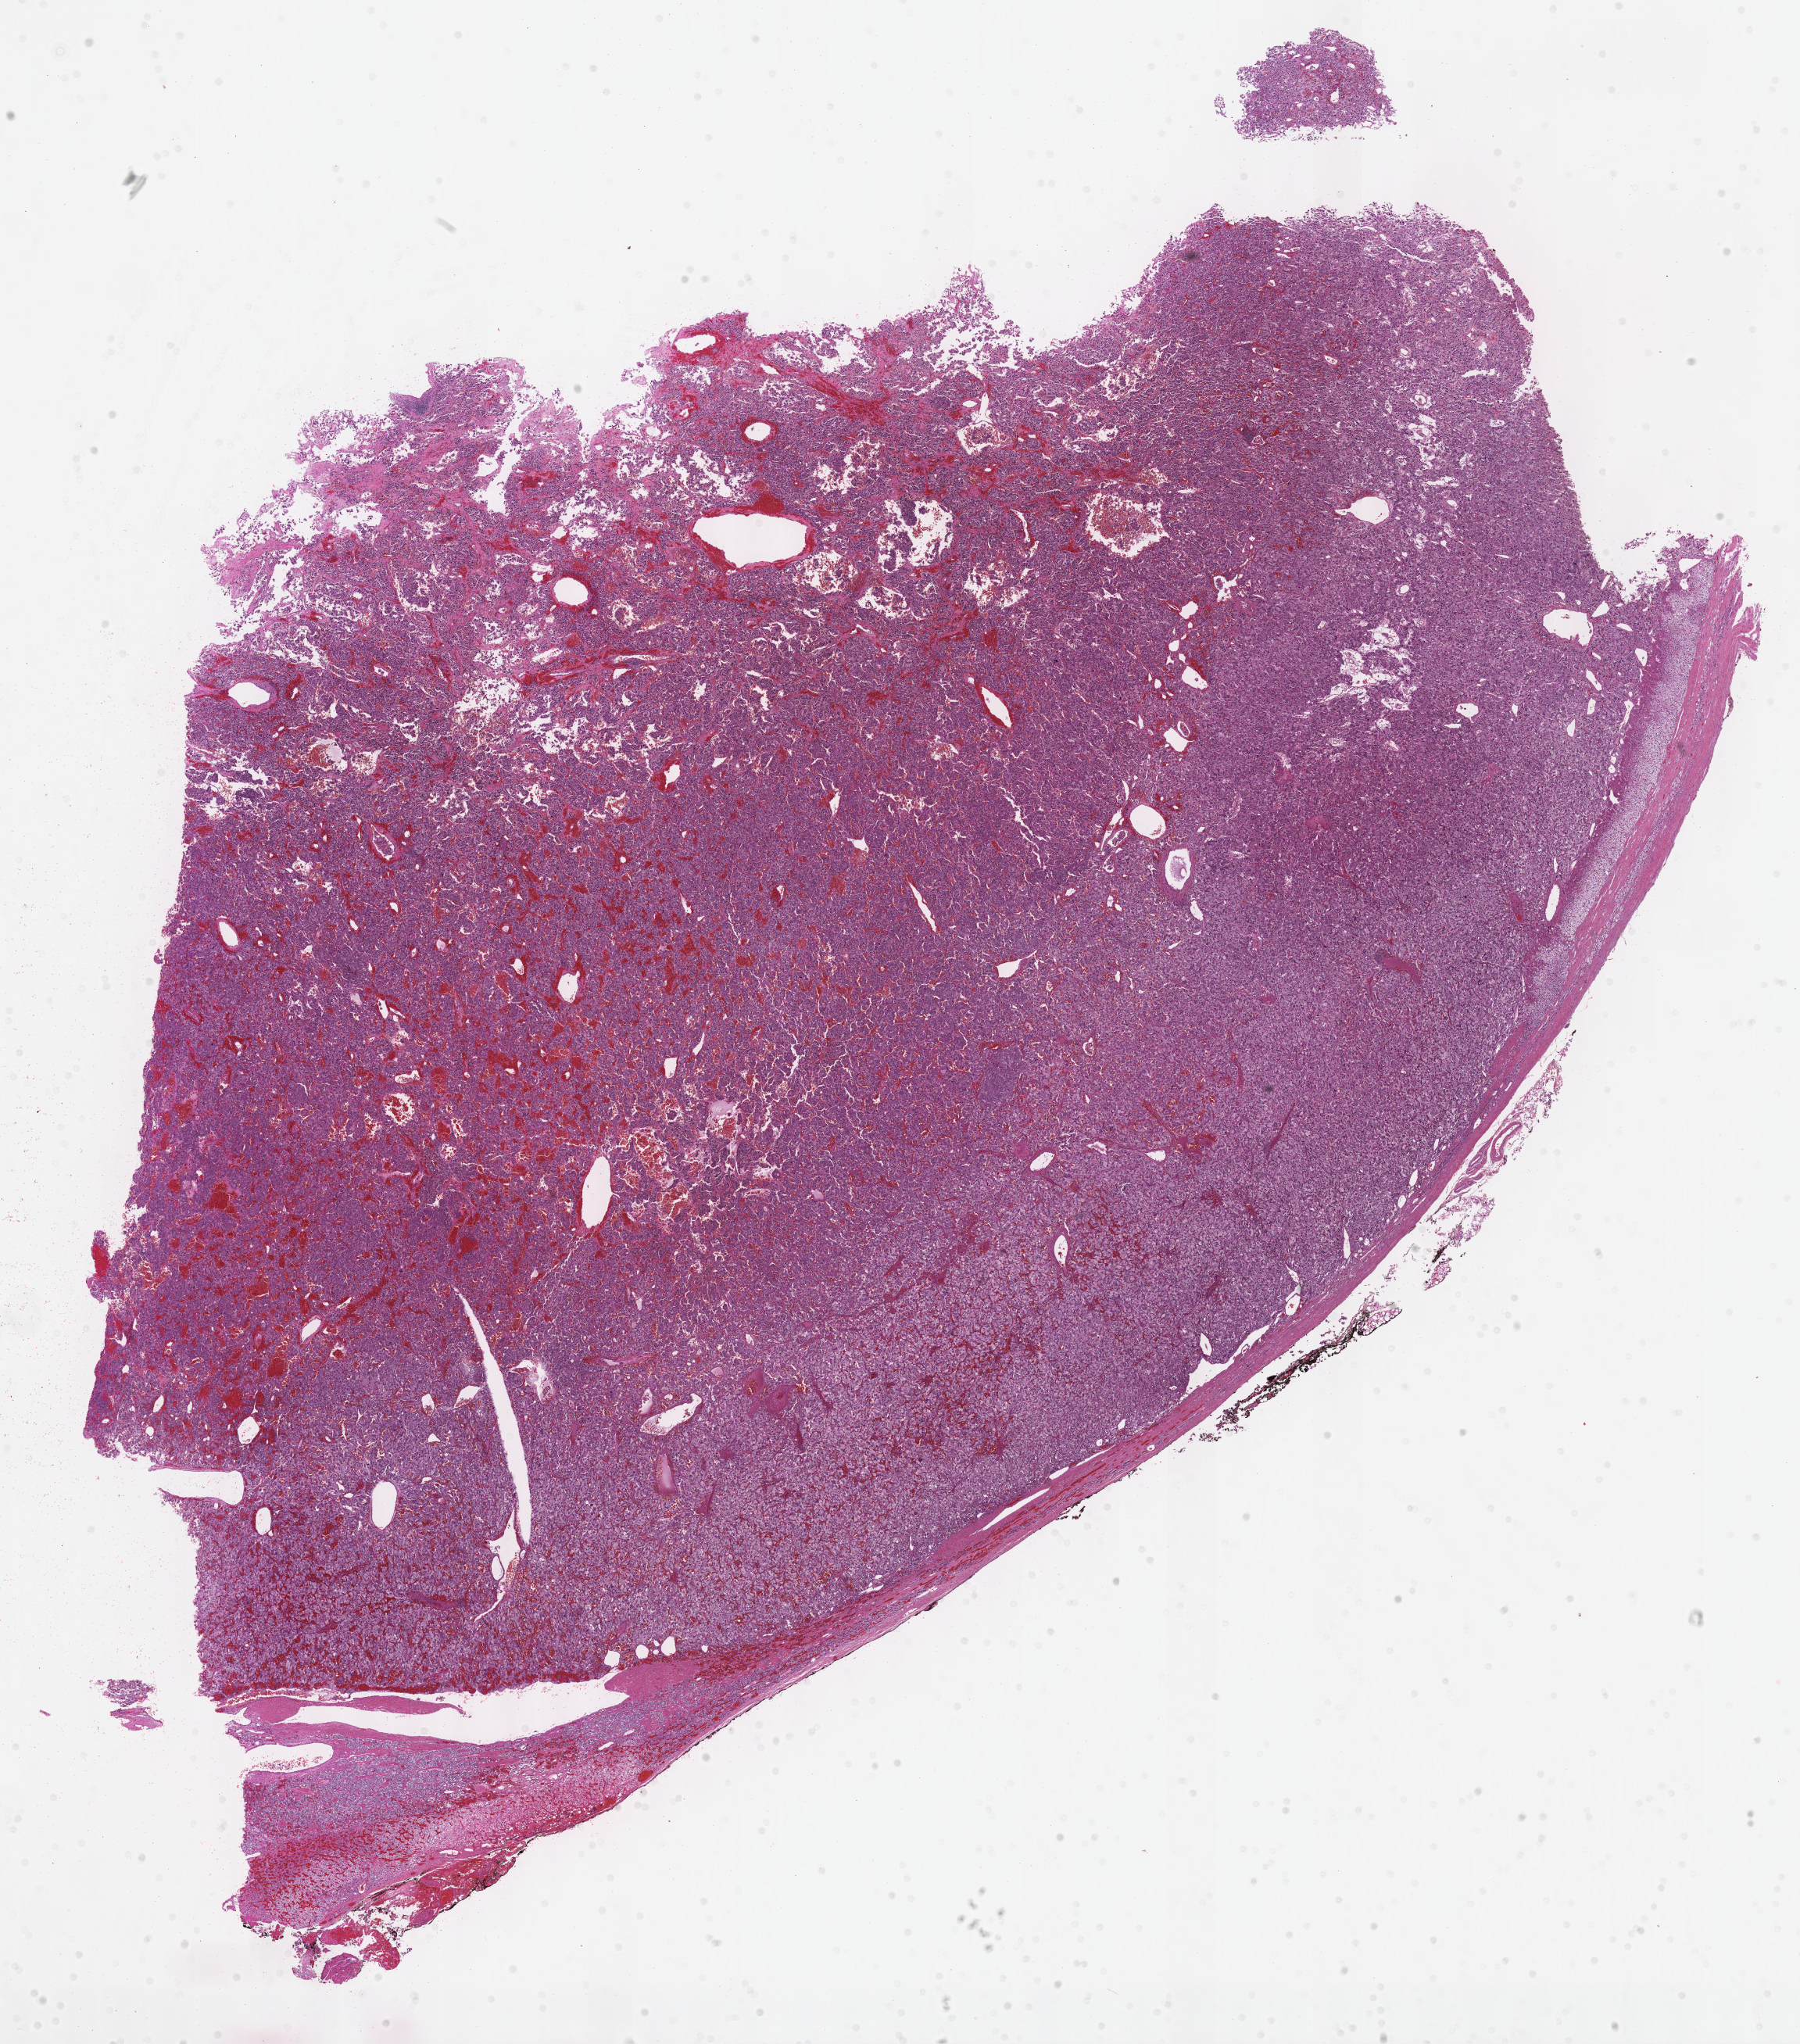
Digitized Hematoxylin and eosin (H&E) stained tissue section (whole slide) — low-resolution overview of the scanned area, about 18.6 x 21.1 mm (acquisition: 40x scan). FFPE section. Primary tumour sample from the adrenal gland. Patient: male, age at initial diagnosis 43 years.
• pathologic diagnosis: Pheochromocytoma, malignant